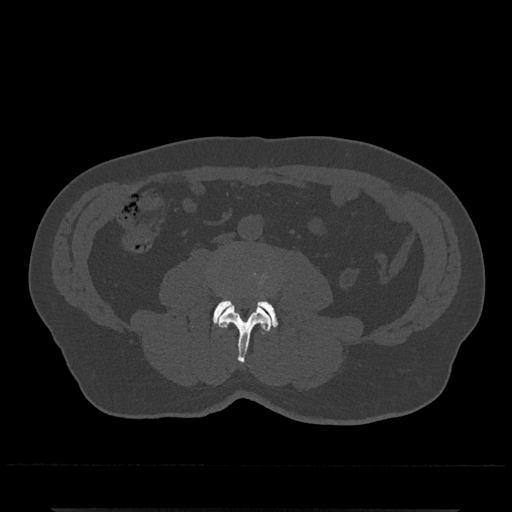
CT including the spine, one axial slice. Slice 196 of 797 in the series (ordered by position). 120 kVp. Bone window (W 1800 / L 400 HU). 512 × 512 image matrix, field of view 393 × 393 mm. Patient: male, 67 years. From the clinical record (not read from this slice): primary cancer: prostate.
Outlined on this slice (semi-automatic segmentation, software-assisted and operator-edited):
- L3 vertebra: bounding box <212,274,272,364> (left, top, right, bottom; pixels)
- L4 vertebra: <213,299,278,327>